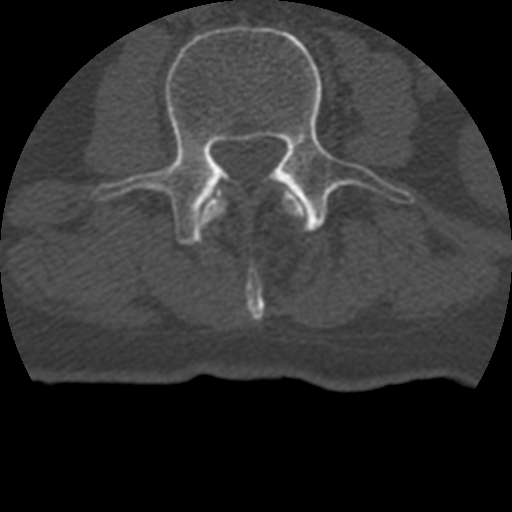
CT including the spine, one axial slice. 120 kVp. Bone window (W 1800 / L 400 HU). 1.25 mm slice thickness. 512 × 512 image matrix, field of view 160 × 160 mm. Patient age 69 years. Case-level facts recorded for this patient, not image findings: primary cancer: prostate.
Structures marked on this image (semi-automatically segmented with operator editing):
- L2 vertebra: bounding box (x1, y1, x2, y2) in pixels: (202, 193, 305, 320)
- L3 vertebra: (78, 25, 412, 245)